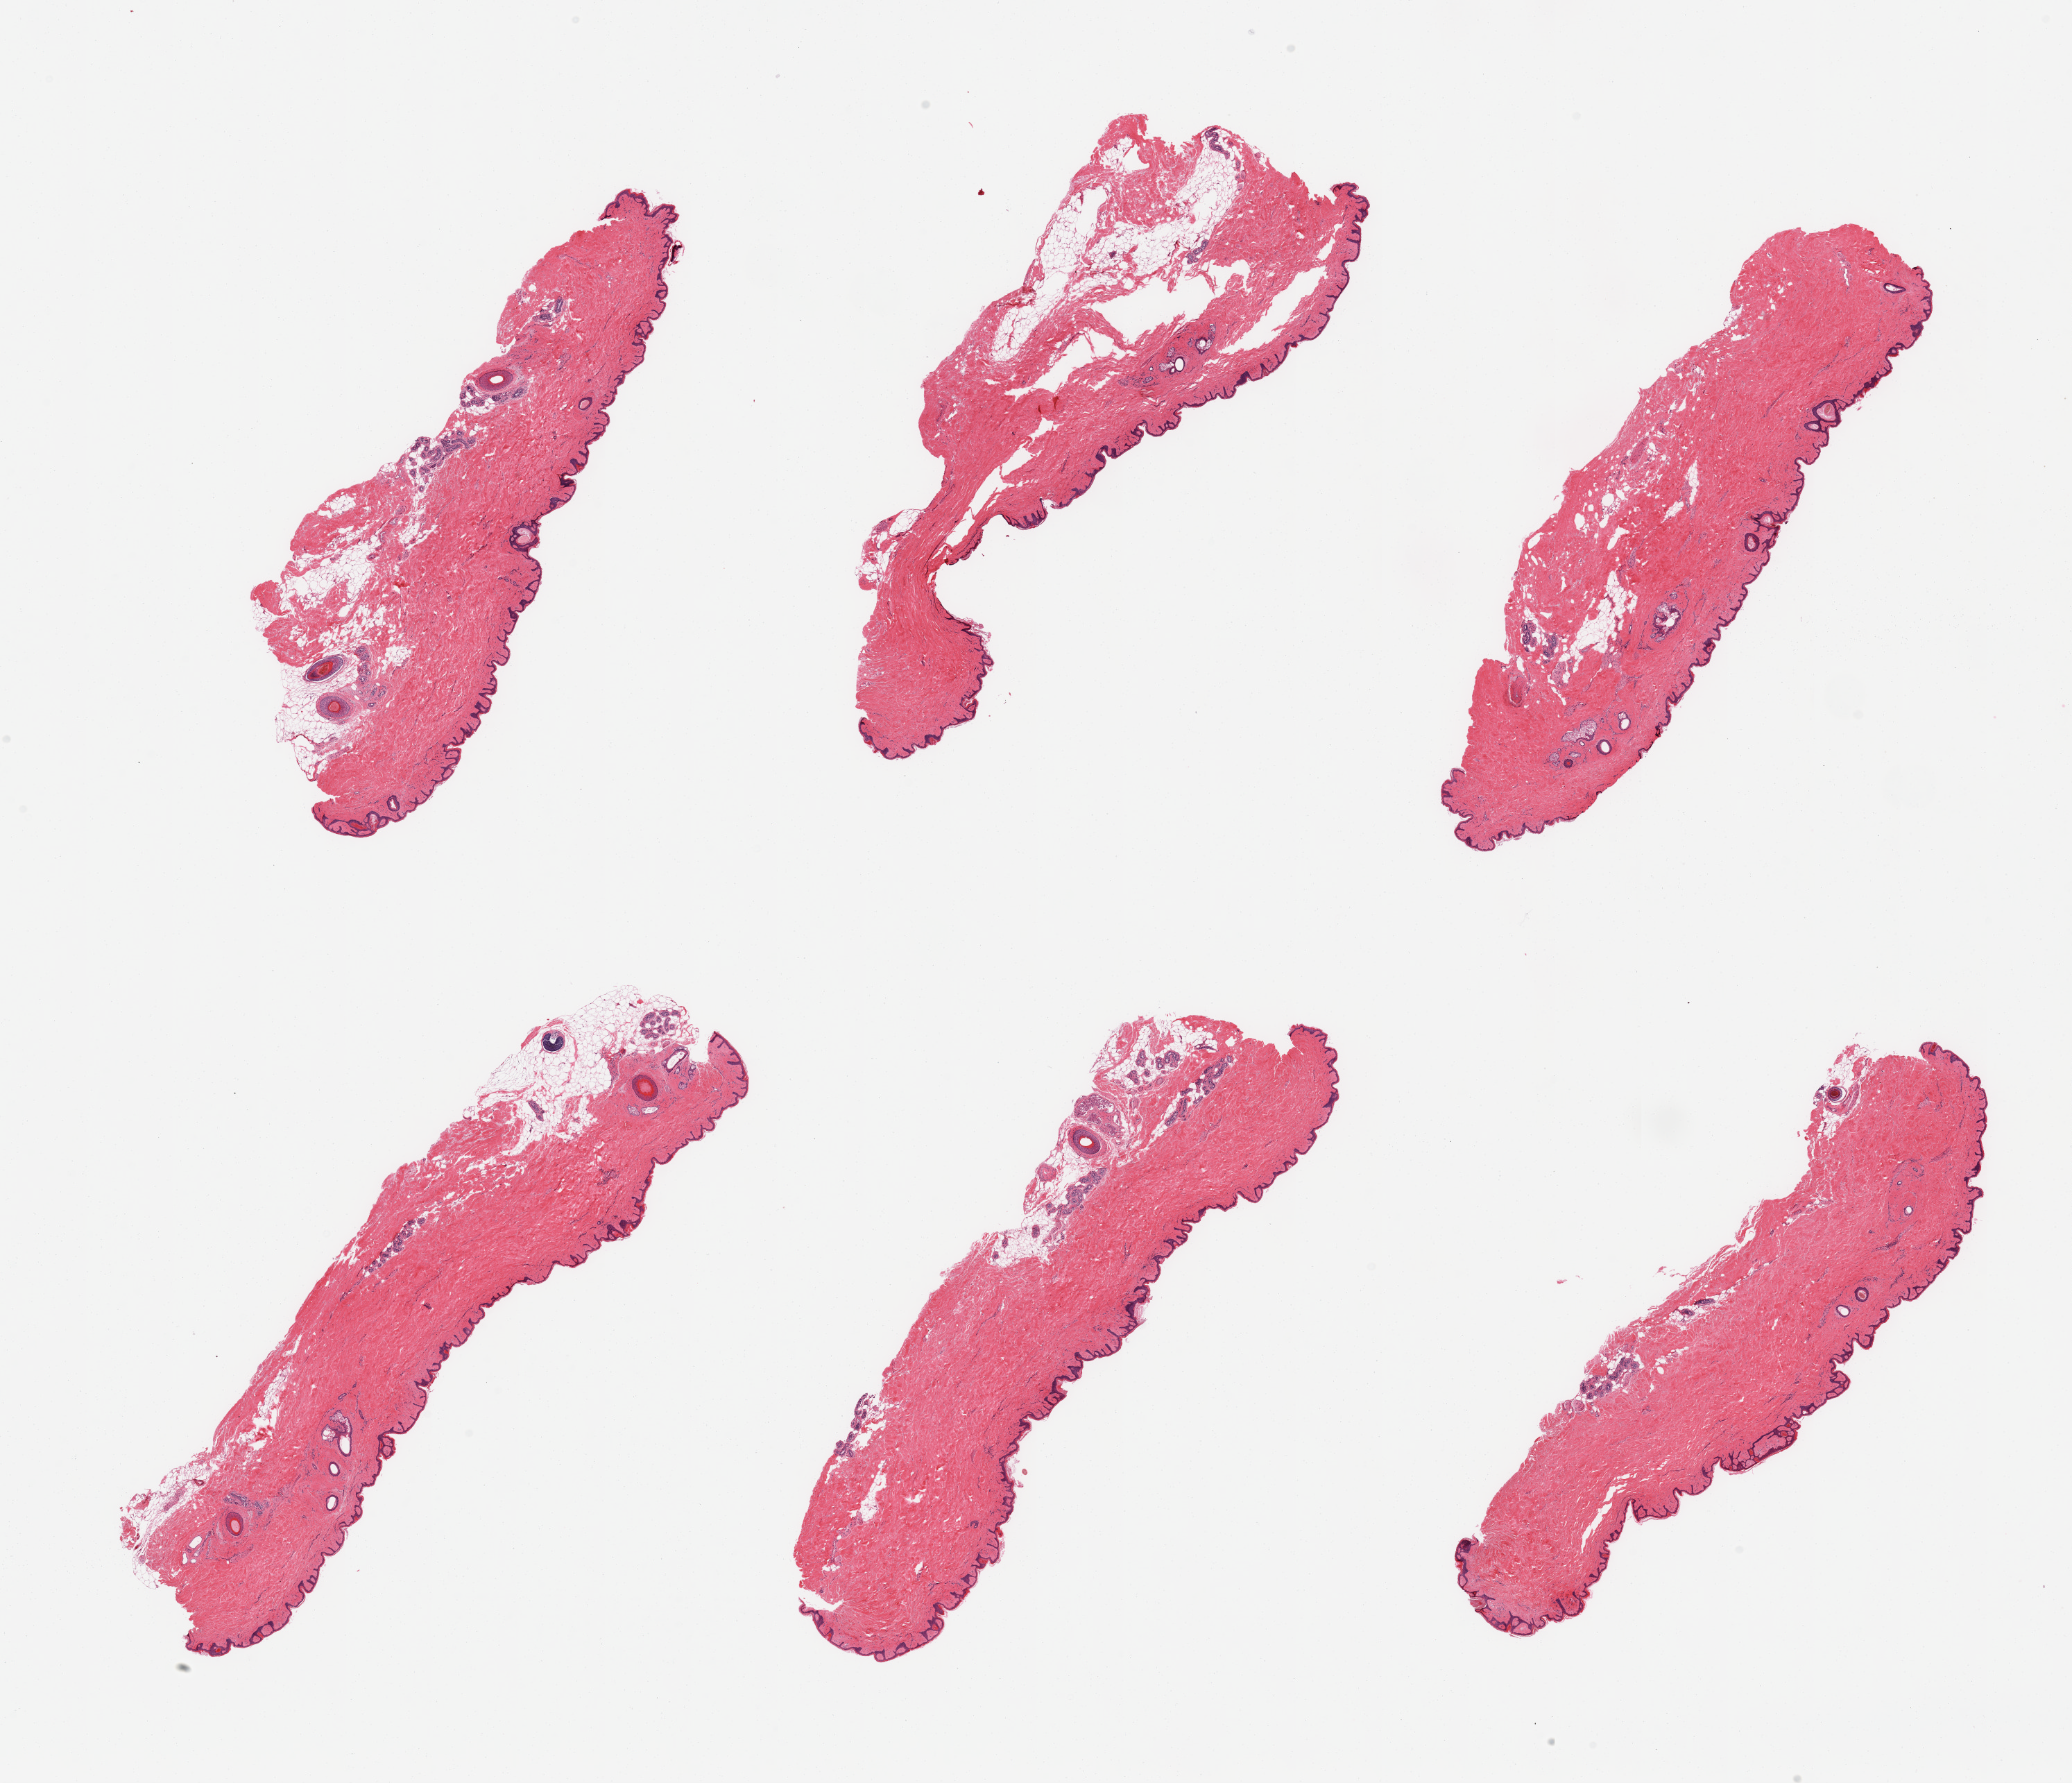
Digitized hematoxylin and eosin (H&E)-stained section, brightfield, a low-resolution overview of the entire scanned area, about 23.6 x 20.3 mm (slide scanned at 20x); PAXgene-fixed, paraffin-embedded tissue; section of skin of suprapubic region (target tissue); tissue donor sample.
Review note (as recorded): 6 pieces, minimal dermal fat, focal nubbin; squamous epithelium is ~30-40 microns.